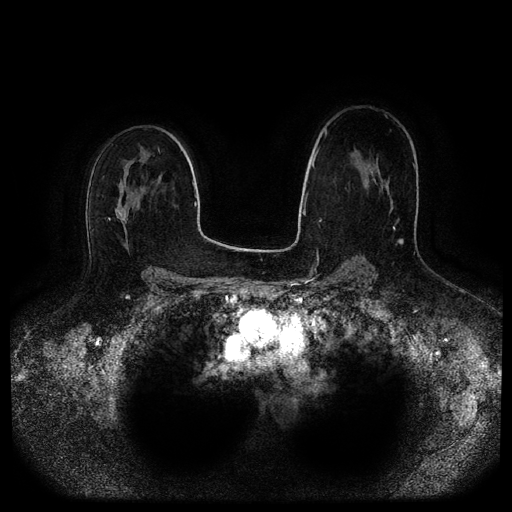
Breast MRI (dynamic contrast-enhanced, multi-phase), one axial slice; slice 61 of 116 in the series (ordered by position); dynamic contrast-enhanced series, time point 2 of 5 at this slice position (early post-contrast); 1.5 T; TE 2.6 ms, TR 5.2 ms; 512 × 512 image matrix, field of view 380 × 380 mm. Patient: female, 45 years.
Annotated regions visible in this slice (semi-automatically segmented with operator editing):
- breast lesion (labelled benign in the annotation): bounding box (x1, y1, x2, y2) in pixels: (364, 180, 368, 189)